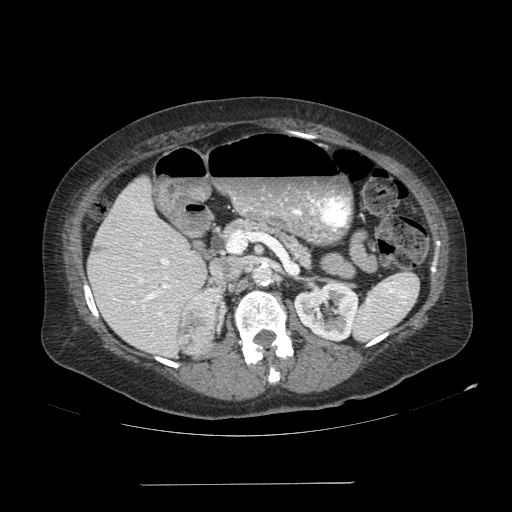
Contrast-enhanced abdominal CT, one axial slice; position 56 of 113 along the scan axis; soft-tissue window (W 400 / L 40 HU); 2.5 mm slice thickness; 512 × 512 image matrix, field of view 440 × 440 mm. Female patient, age 67 years. Case-level facts recorded for this patient, not image findings: diagnosis: adrenocortical carcinoma; tumour side: right adrenal; tumour size at pathology: 9.8 cm; Ki-67 index: 59 %.
Structures marked on this image (semi-automatic segmentation, software-assisted and operator-edited):
- mass: box from (x=178, y=289) to (x=222, y=352) px